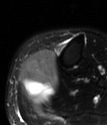
MRI of an extremity soft-tissue mass, one axial slice; position 24 of 78 along the scan axis; T2-weighted fat-saturated; MR volume resampled by the dataset authors to the PET/CT grid (not the native acquisition matrix); 3.27 mm slice thickness; 107 × 125 image matrix, field of view 104 × 122 mm. Female patient. Case-level facts recorded for this patient, not image findings: histological type: extraskeletal high grade osteogenic sarcoma; grade: high; site of the primary tumour: left calf.
Structures marked on this image (expert contour drawn on MRI and transferred to this co-registered scan by the dataset authors):
- gross tumour volume (mass): bounding box <19,50,59,105> (left, top, right, bottom; pixels)